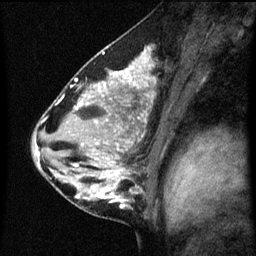
Breast MRI (dynamic contrast-enhanced), one sagittal slice; dynamic contrast-enhanced series, image 2 of 3 at this slice position (ordered by acquisition); 1.5 T; TE 4.2 ms, TR 8 ms; 2.3 mm slice thickness; 256 × 256 image matrix. Patient: female, 33 years.
Structures marked on this image (semi-automatically segmented with operator editing):
- analysis volume of interest (the breast-tissue region the enhancement analysis was run in; not a lesion): box from (x=71, y=118) to (x=145, y=209) px
- tumour enhancement mask (voxels above the 70 % enhancement threshold inside the analysis volume of interest): (x=74, y=162)–(x=128, y=209)